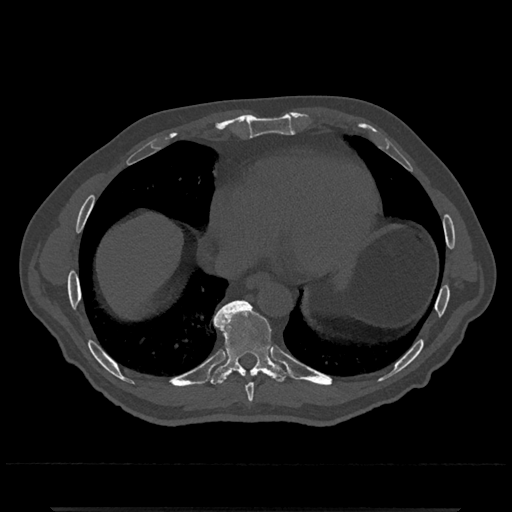
CT including the spine, one axial slice. Slice 629 of 797 in the series (ordered by position). Reconstruction kernel Br40s/3. Bone window (W 1800 / L 400 HU). 512 × 512 image matrix, field of view 393 × 393 mm. Patient: male, 67 years. Case-level facts recorded for this patient, not image findings: primary cancer: prostate.
Annotated regions visible in this slice (semi-automatic segmentation, software-assisted and operator-edited):
- T8 vertebra: bounding box [x1, y1, x2, y2] px = [246, 383, 254, 403]
- T9 vertebra: [207, 301, 291, 386]